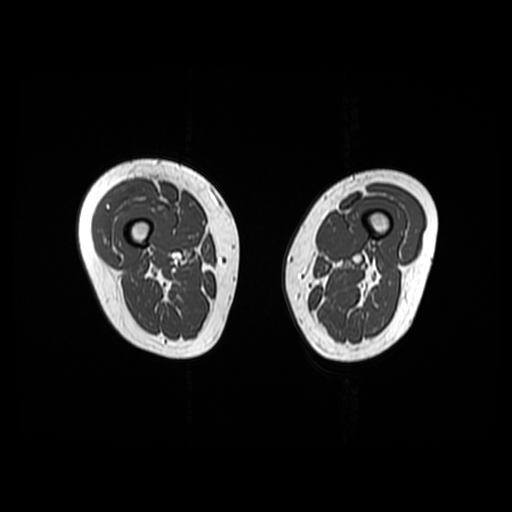
MRI of an extremity soft-tissue mass, one axial slice; slice 13 of 48 in the series (ordered by position); 6 mm slice thickness; 512 × 512 image matrix, field of view 440 × 440 mm. Female patient. Case-level facts recorded for this patient, not image findings: histological type: pleiomorphic undifferentiated sarcoma; grade: high; site of the primary tumour: right quadricep.
Outlined on this slice (outlined manually by an expert reader):
- gross tumour volume including surrounding oedema: bounding box <92,178,157,250> (left, top, right, bottom; pixels)